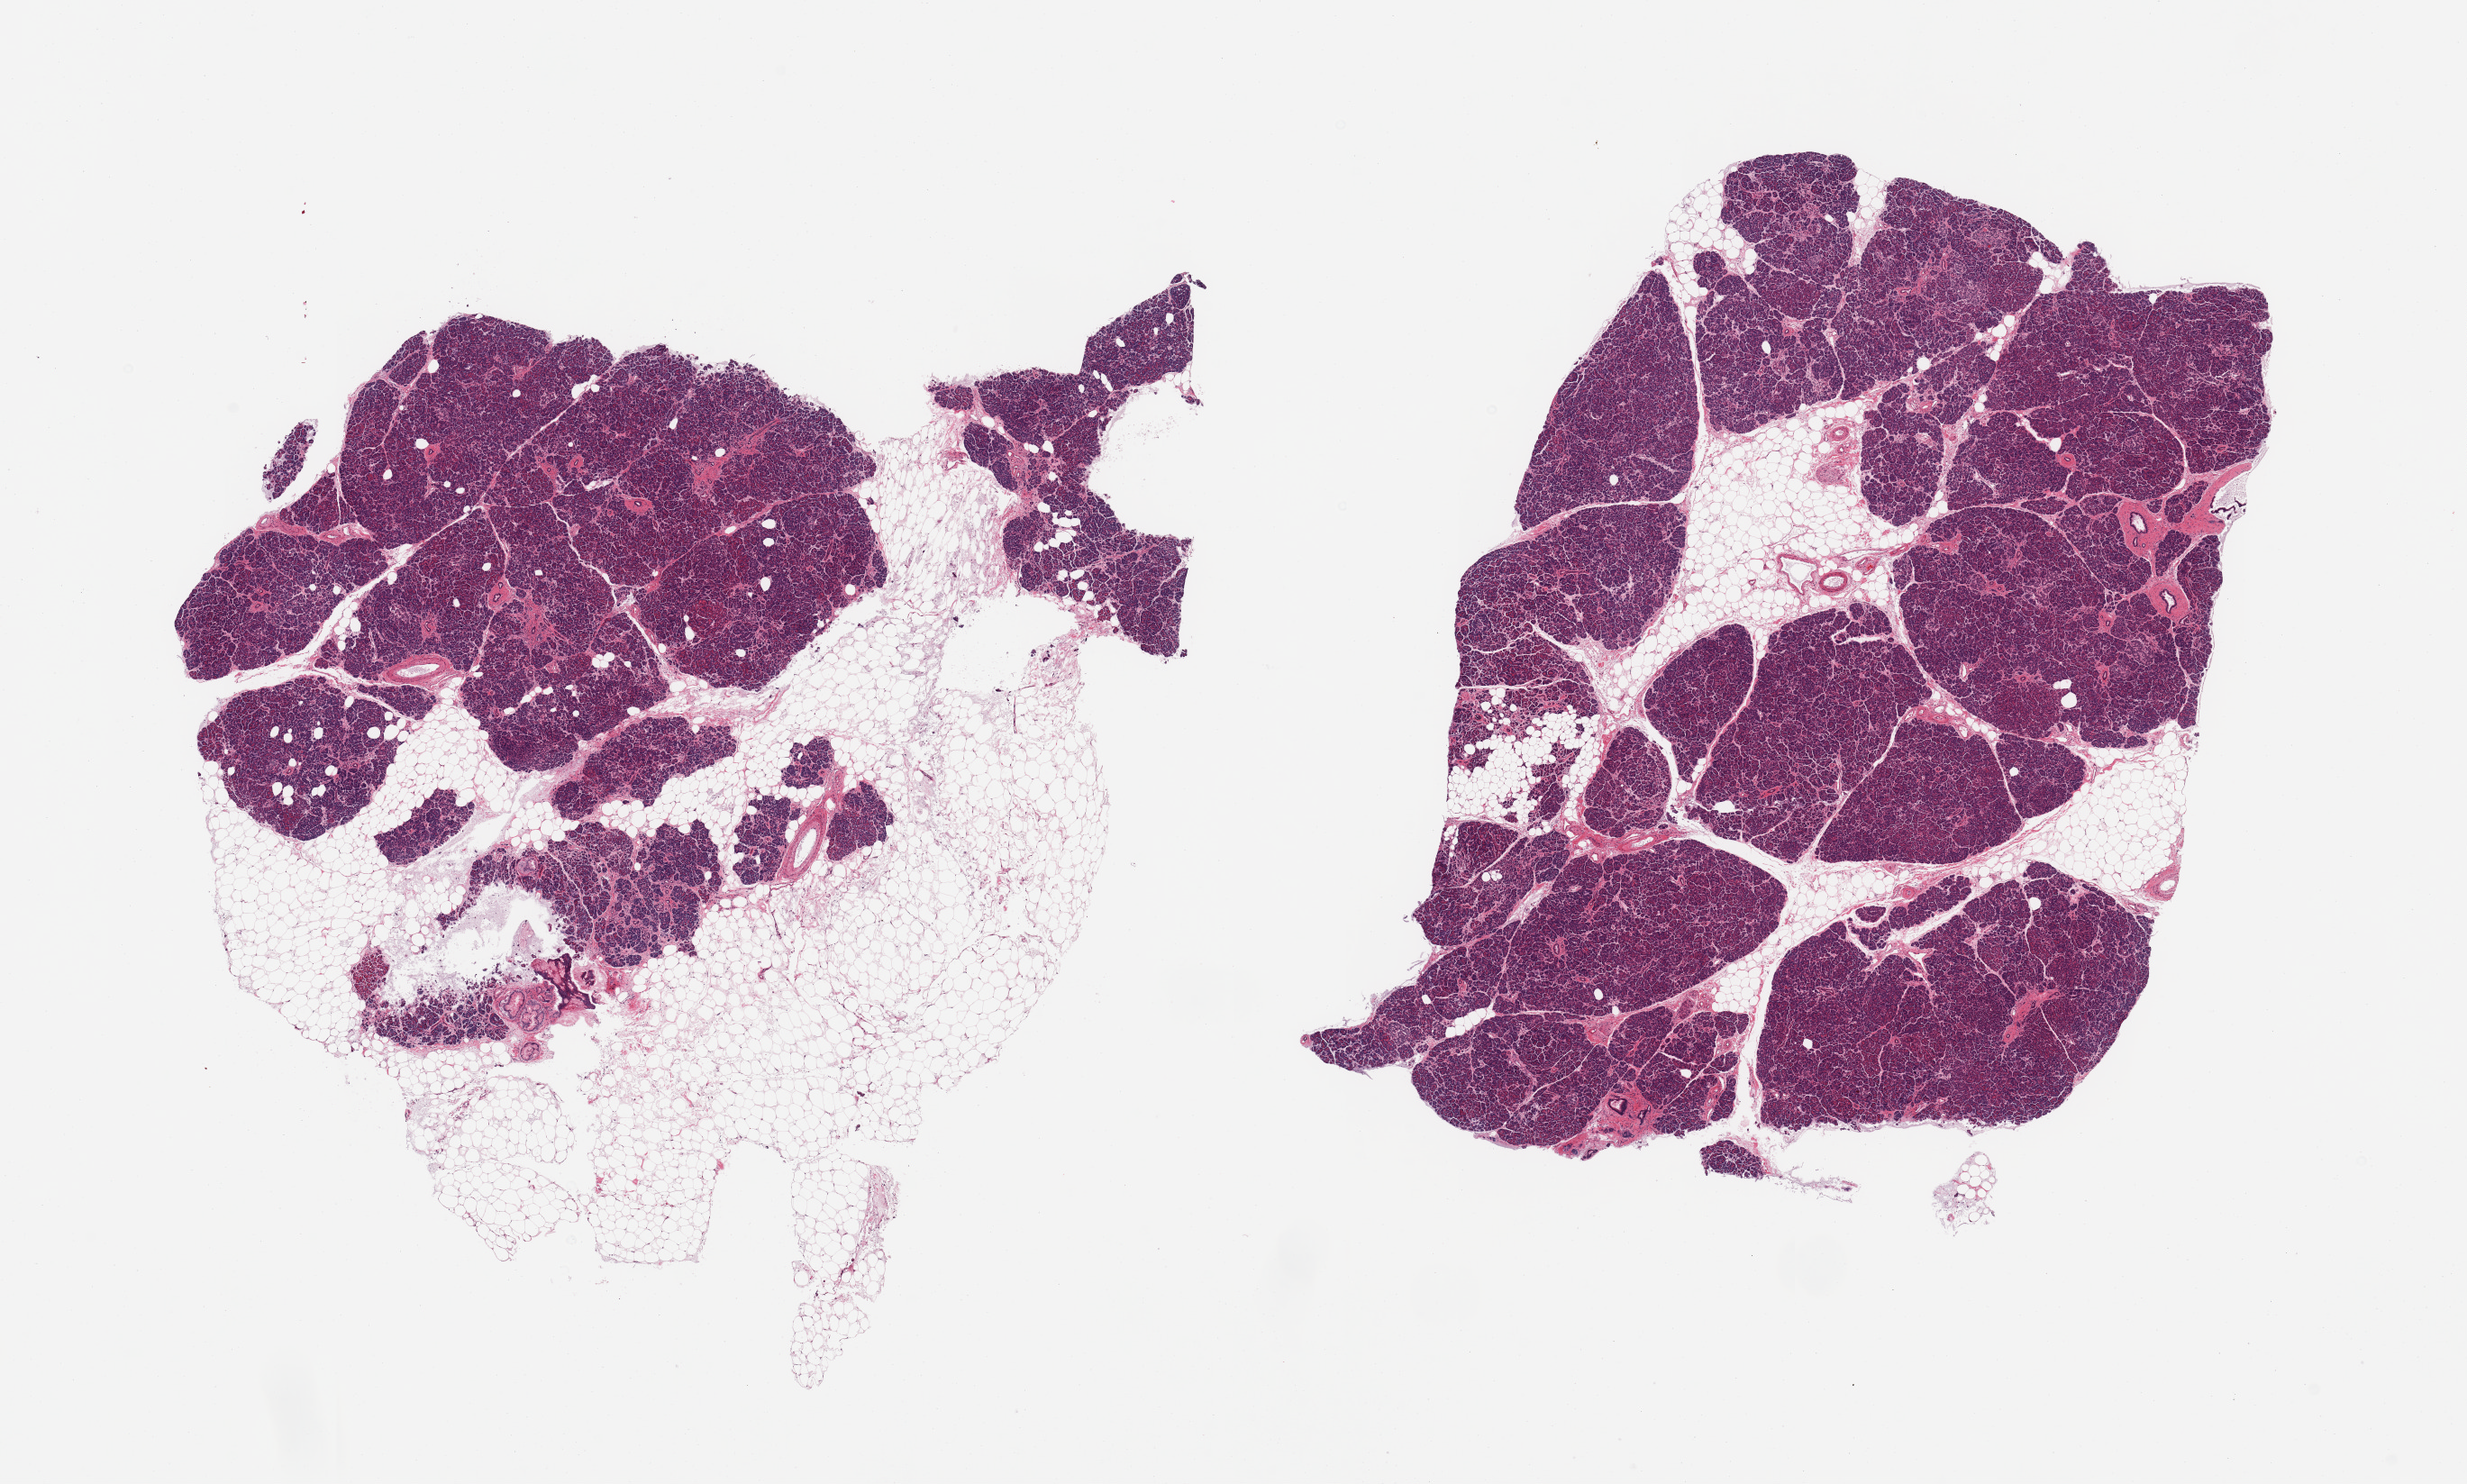
Hematoxylin and eosin (H&E) whole-slide image — shown as a low-resolution overview of the whole scanned area (about 21.7 x 13.0 mm, slide scanned at 20x). PAXgene-fixed, paraffin-embedded tissue. Target tissue: pancreas. Tissue donor sample. Male donor.
• review note (as recorded): 2 pieces; ~10 to 50% external/internal fat, mildly autolyzed parenchyma with well visualized islets, fragment with focal PanIN-1